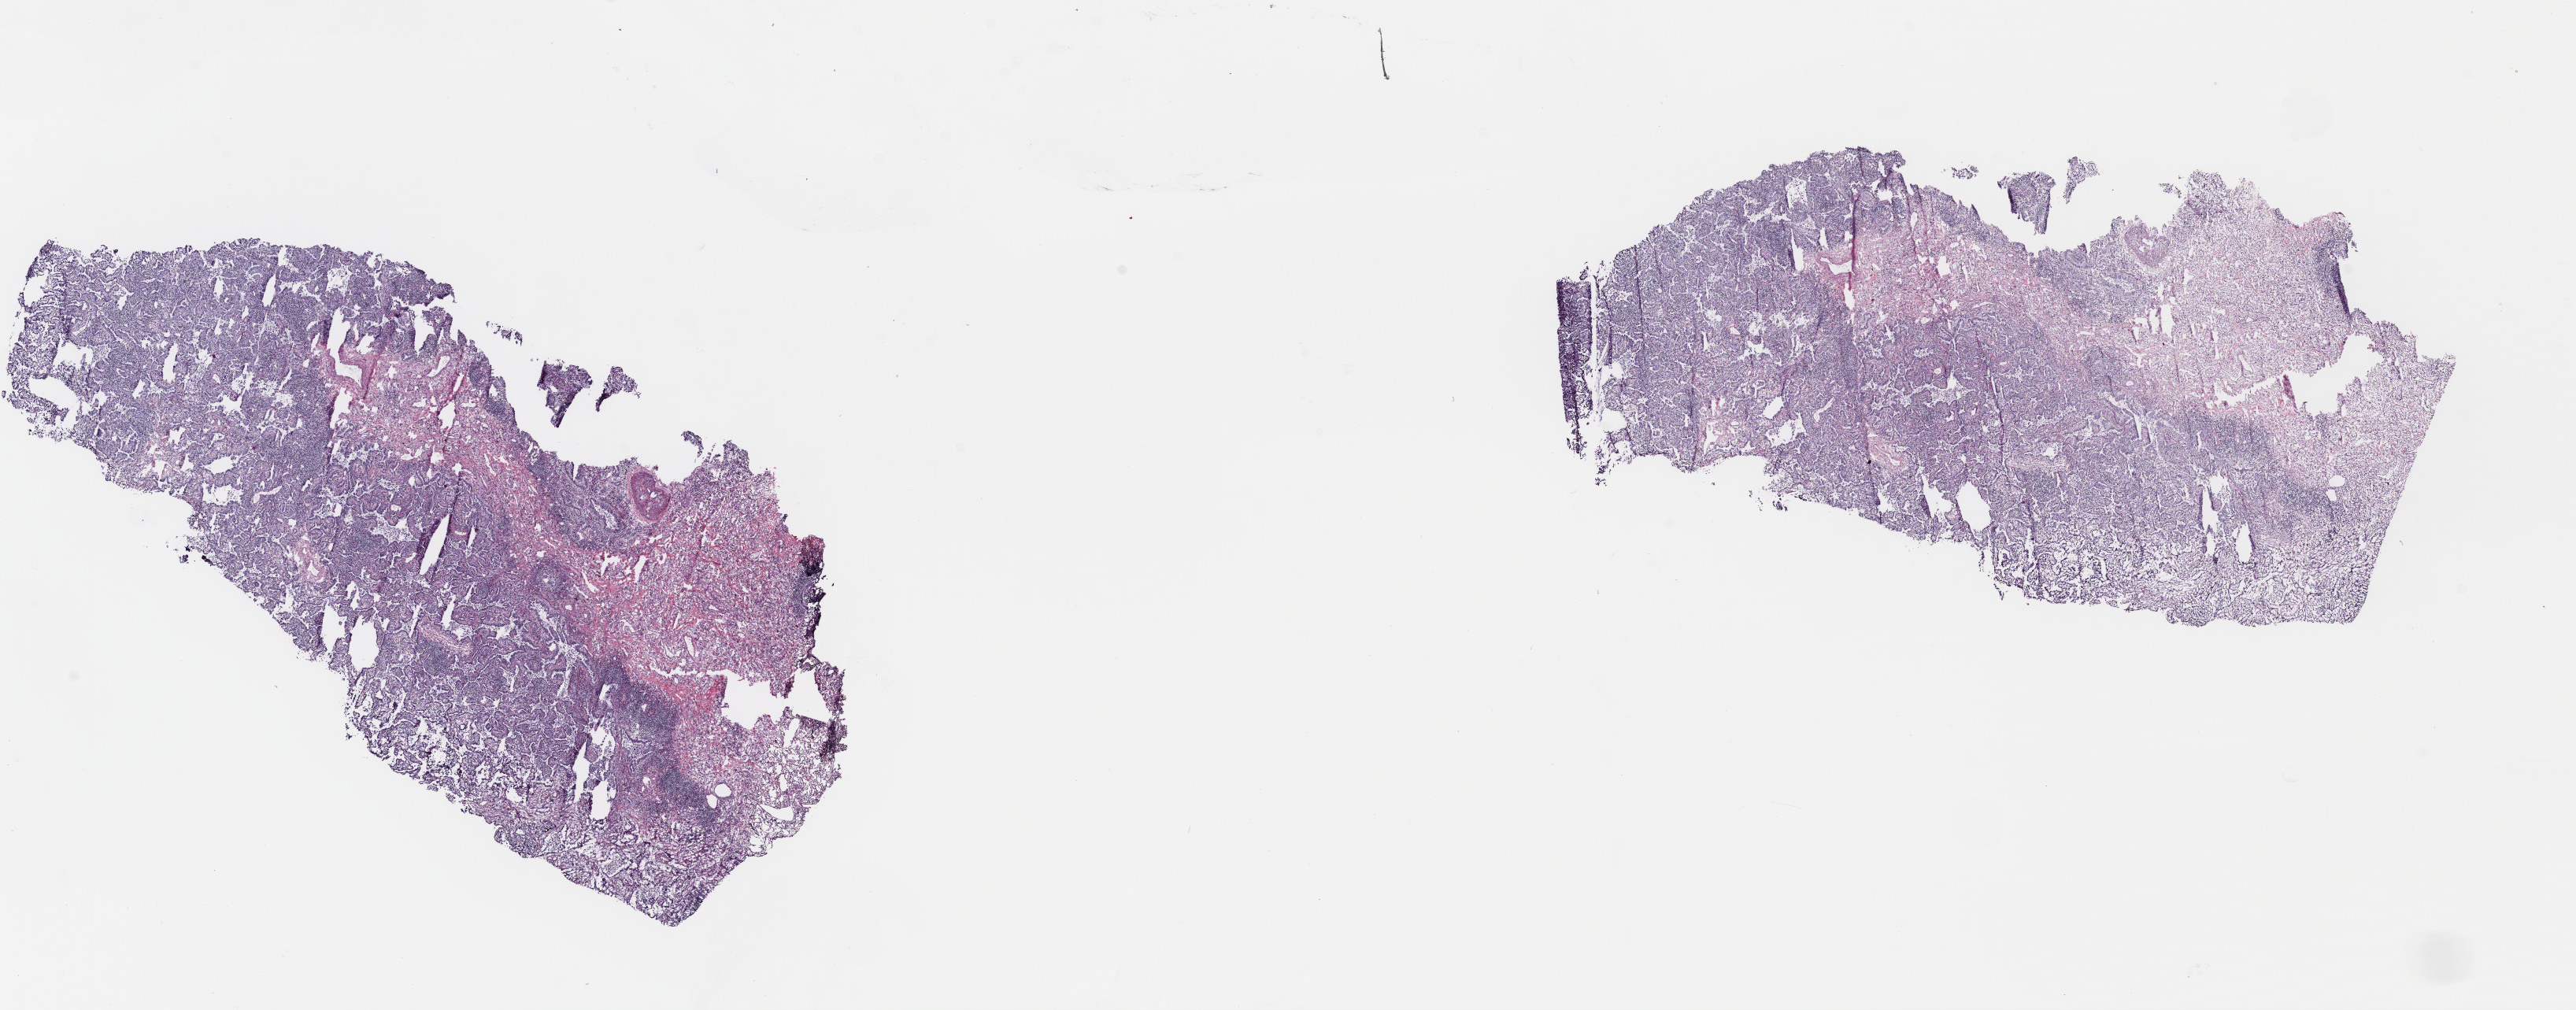
Digitized H&E-stained tissue section (whole slide), low-resolution overview of the scanned area, about 25.7 x 10.1 mm (slide scanned at 40x); frozen section from the top of the tissue portion; sample: primary tumour, lung. Female, age 70 years at initial diagnosis. Pathologist review of this section (percent, as recorded): tumour cells 70%, tumour nuclei 70%.
Pathologic diagnosis: Adenocarcinoma, NOS (lower lobe, lung).